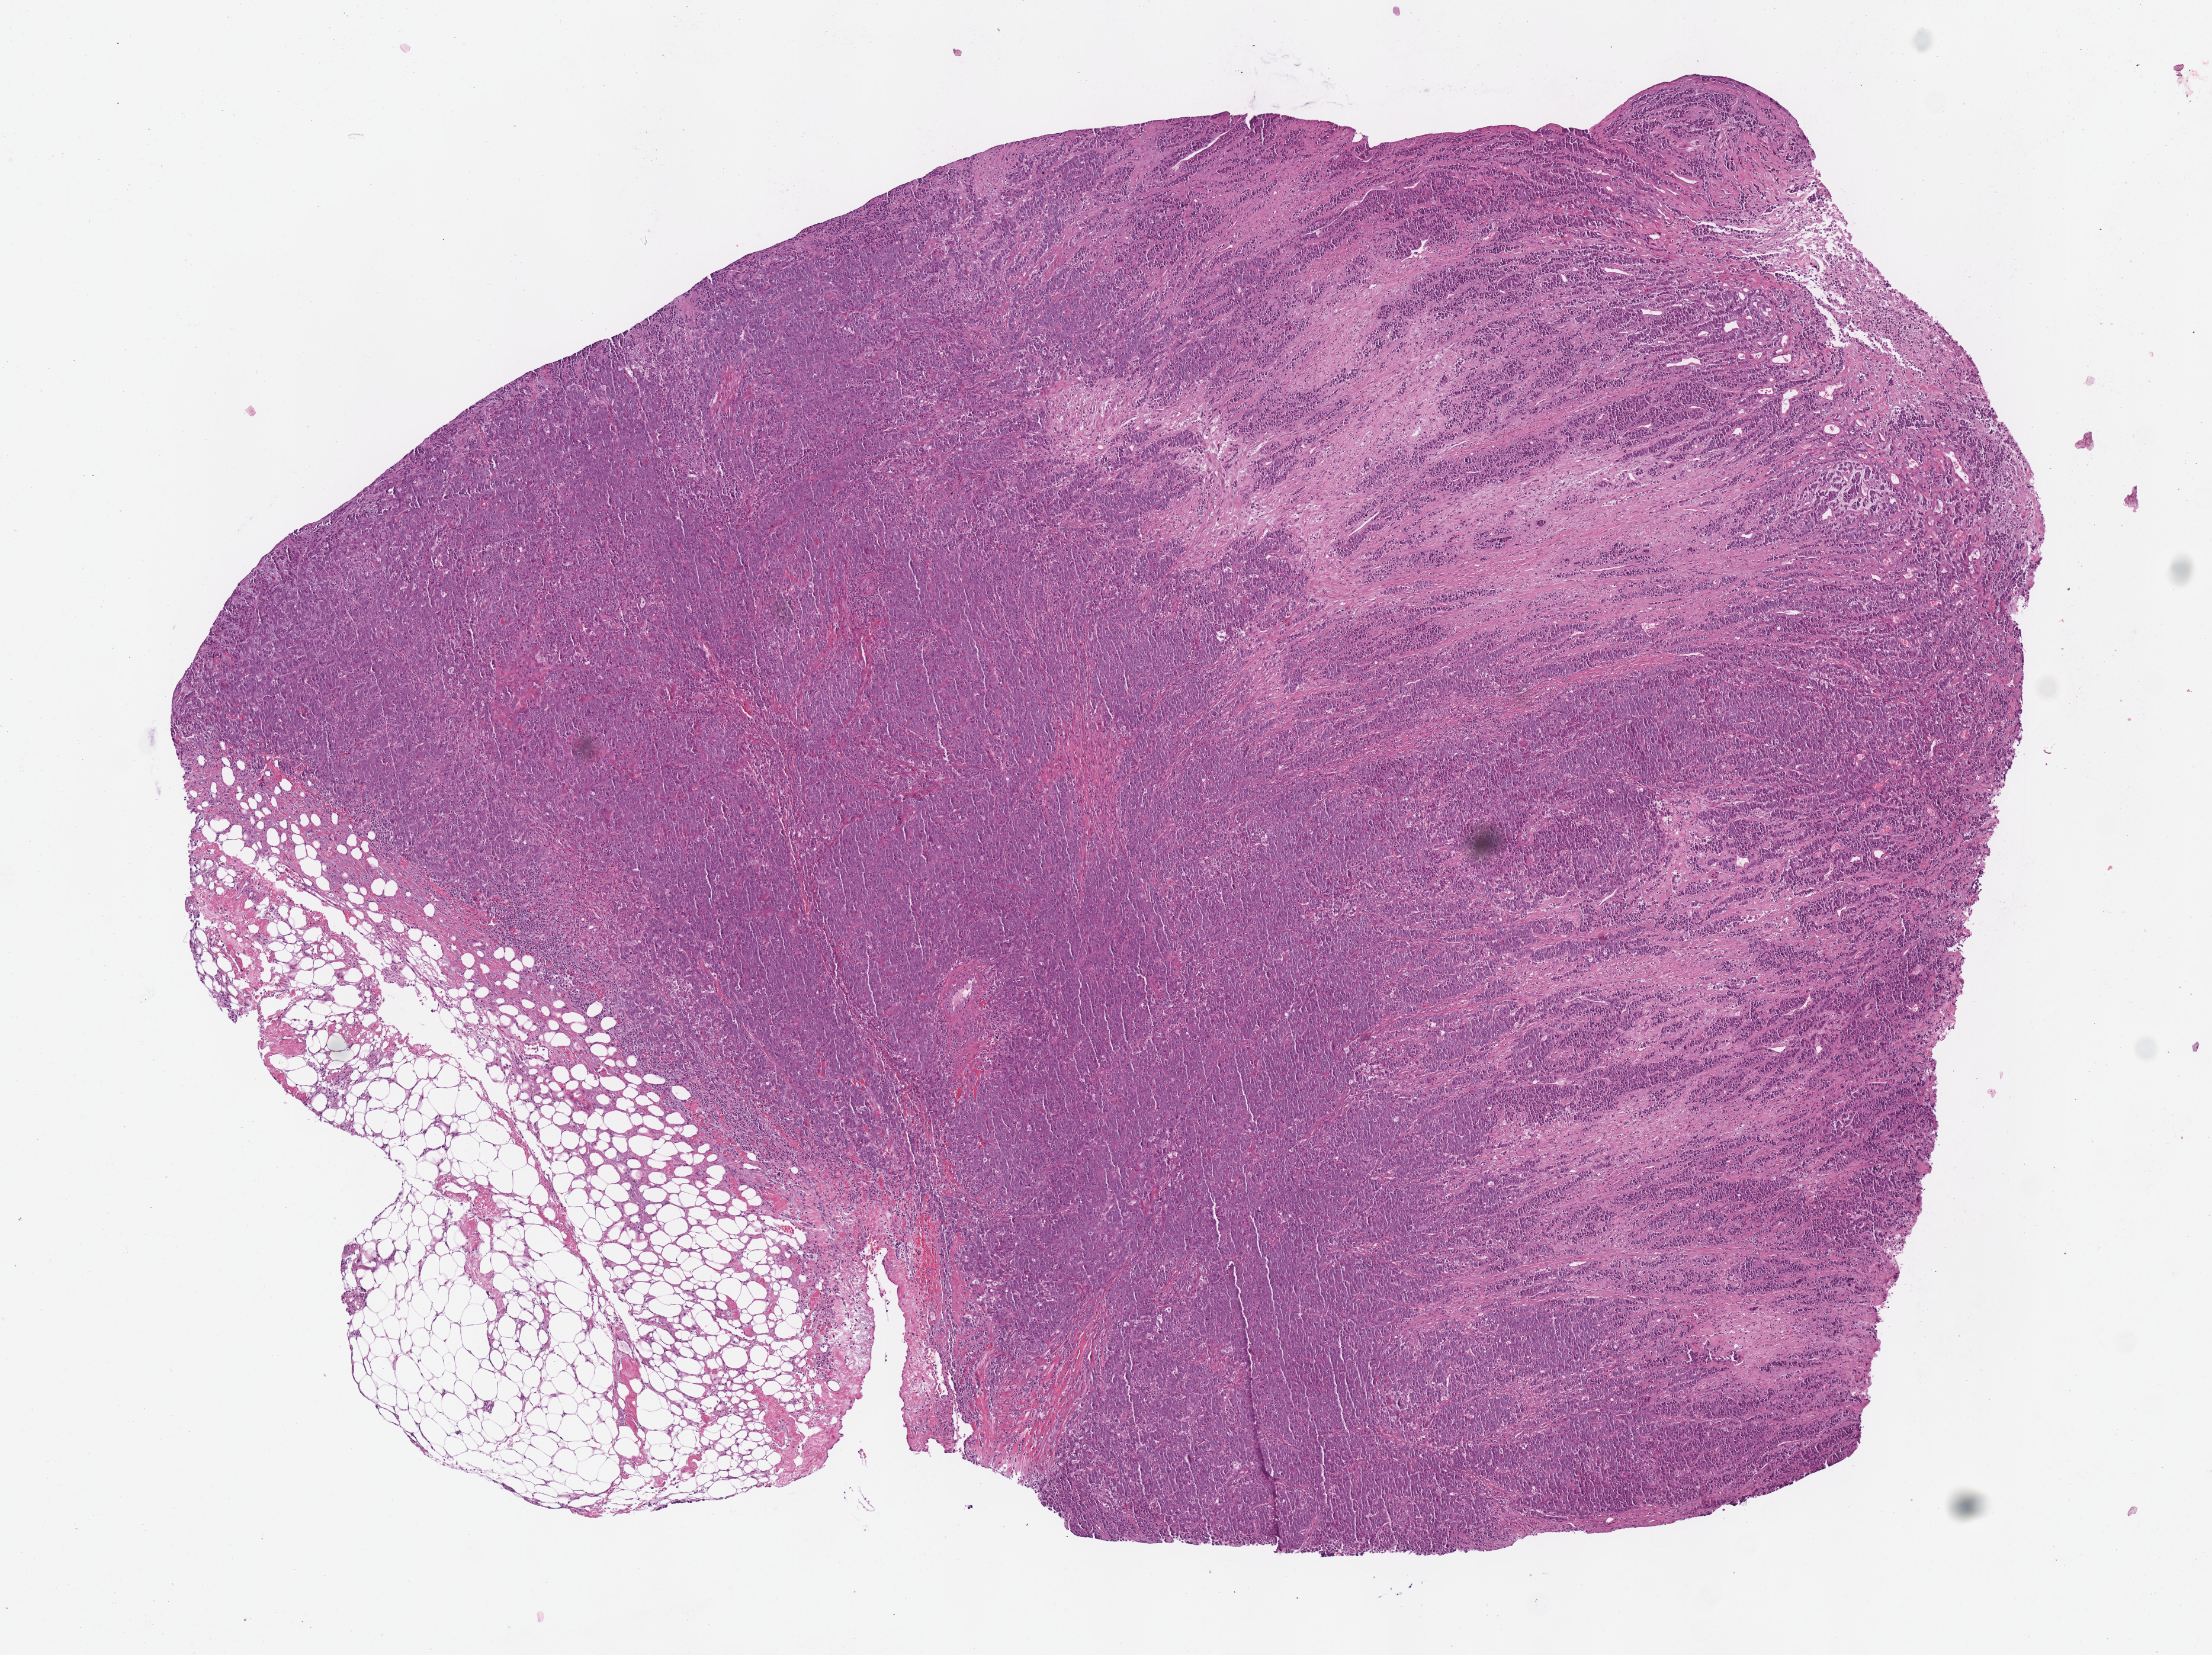
Digitized Hematoxylin and eosin (H&E) stained tissue section (whole slide) — low-resolution overview of the scanned area, about 7.3 x 5.5 mm (slide scanned at 40x), frozen section from the top of the tissue portion, colon, primary tumour sample. Patient: female, age at initial diagnosis 75 years. Pathologist review of this section (percent, as recorded): tumour cells 85%, tumour nuclei 90%, normal cells 5%, stromal cells 7%, necrosis 3%.
Pathologic diagnosis: Adenocarcinoma, NOS. AJCC pathologic stage: IIB (6th edition).